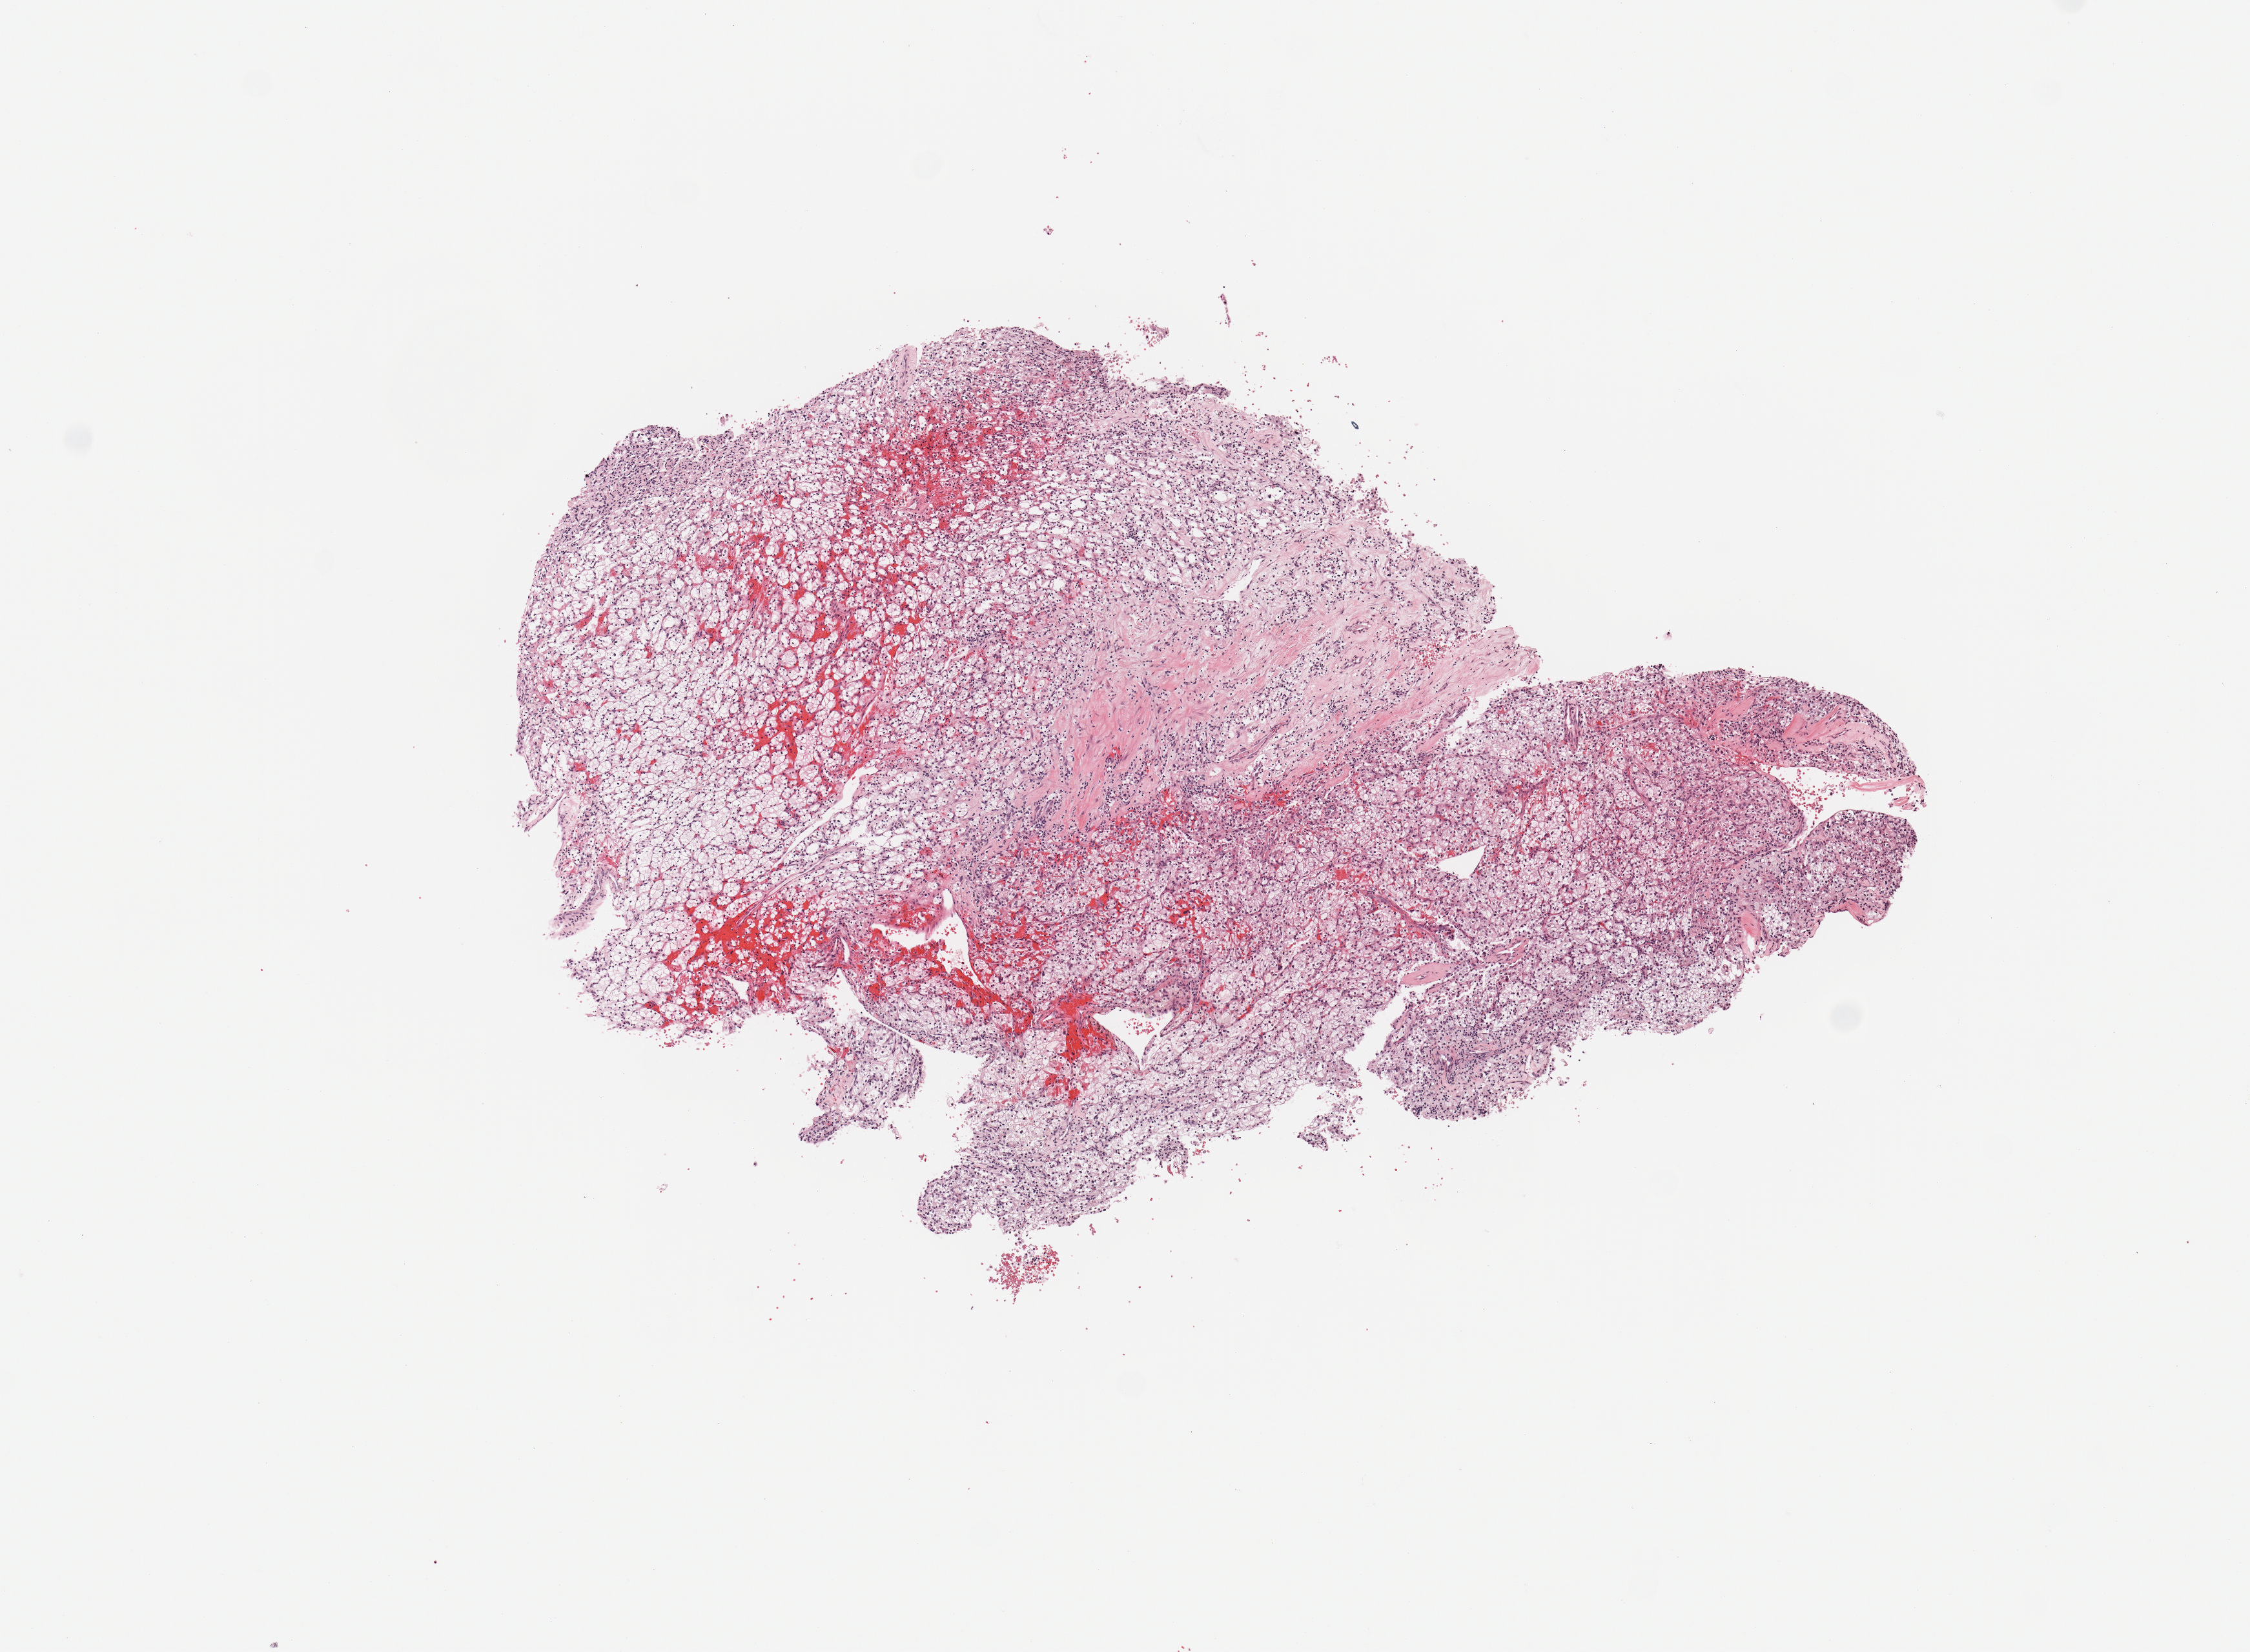
Digitized Hematoxylin and eosin (H&E) stained tissue section (whole slide) — a low-resolution overview of the entire scanned area, about 6.9 x 5.1 mm, normal (non-tumour) tissue sample, kidney. Male, 61 y/o.
* this section: normal (non-tumour) tissue from the same patient
* patient diagnosis: Renal cell carcinoma, NOS